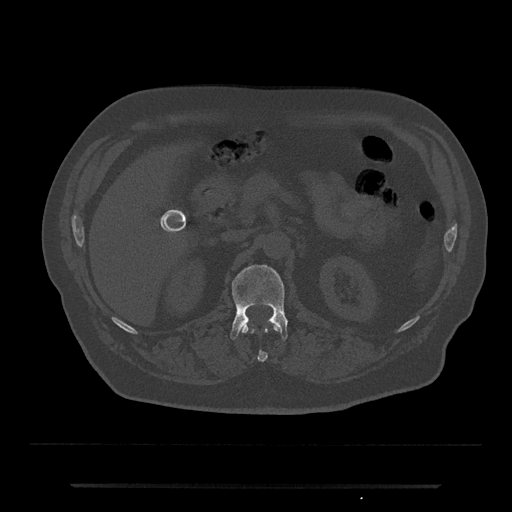
CT including the spine, one axial slice; slice 553 of 797 in the series (ordered by position); reconstruction kernel Br40s/3; bone window (W 1800 / L 400 HU); 0.5 mm slice thickness; 512 × 512 image matrix, field of view 434 × 434 mm. Patient: male, 80 years. Case-level facts recorded for this patient, not image findings: primary cancer: prostate; vertebrae with lytic lesions (as recorded): L1, T11.
Structures marked on this image (semi-automatically segmented with operator editing):
- L1 vertebra: bounding box <230,265,289,339> (left, top, right, bottom; pixels)
- T12 vertebra: <241,324,280,361>